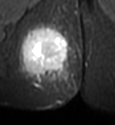
MRI of an extremity soft-tissue mass, one axial slice. STIR. MR volume resampled by the dataset authors to the PET/CT grid (not the native acquisition matrix). 3.27 mm slice thickness. 115 × 125 image matrix, field of view 112 × 122 mm. Female patient. From the clinical record (not read from this slice): histological type: epithelioid sarcoma; grade: intermediate; site of the primary tumour: right buttock.
Annotated regions visible in this slice (expert contour drawn on MRI and transferred to this co-registered scan by the dataset authors):
- gross tumour volume including surrounding oedema: box from (x=17, y=23) to (x=75, y=95) px
- gross tumour volume (mass): (x=22, y=28)–(x=69, y=76)